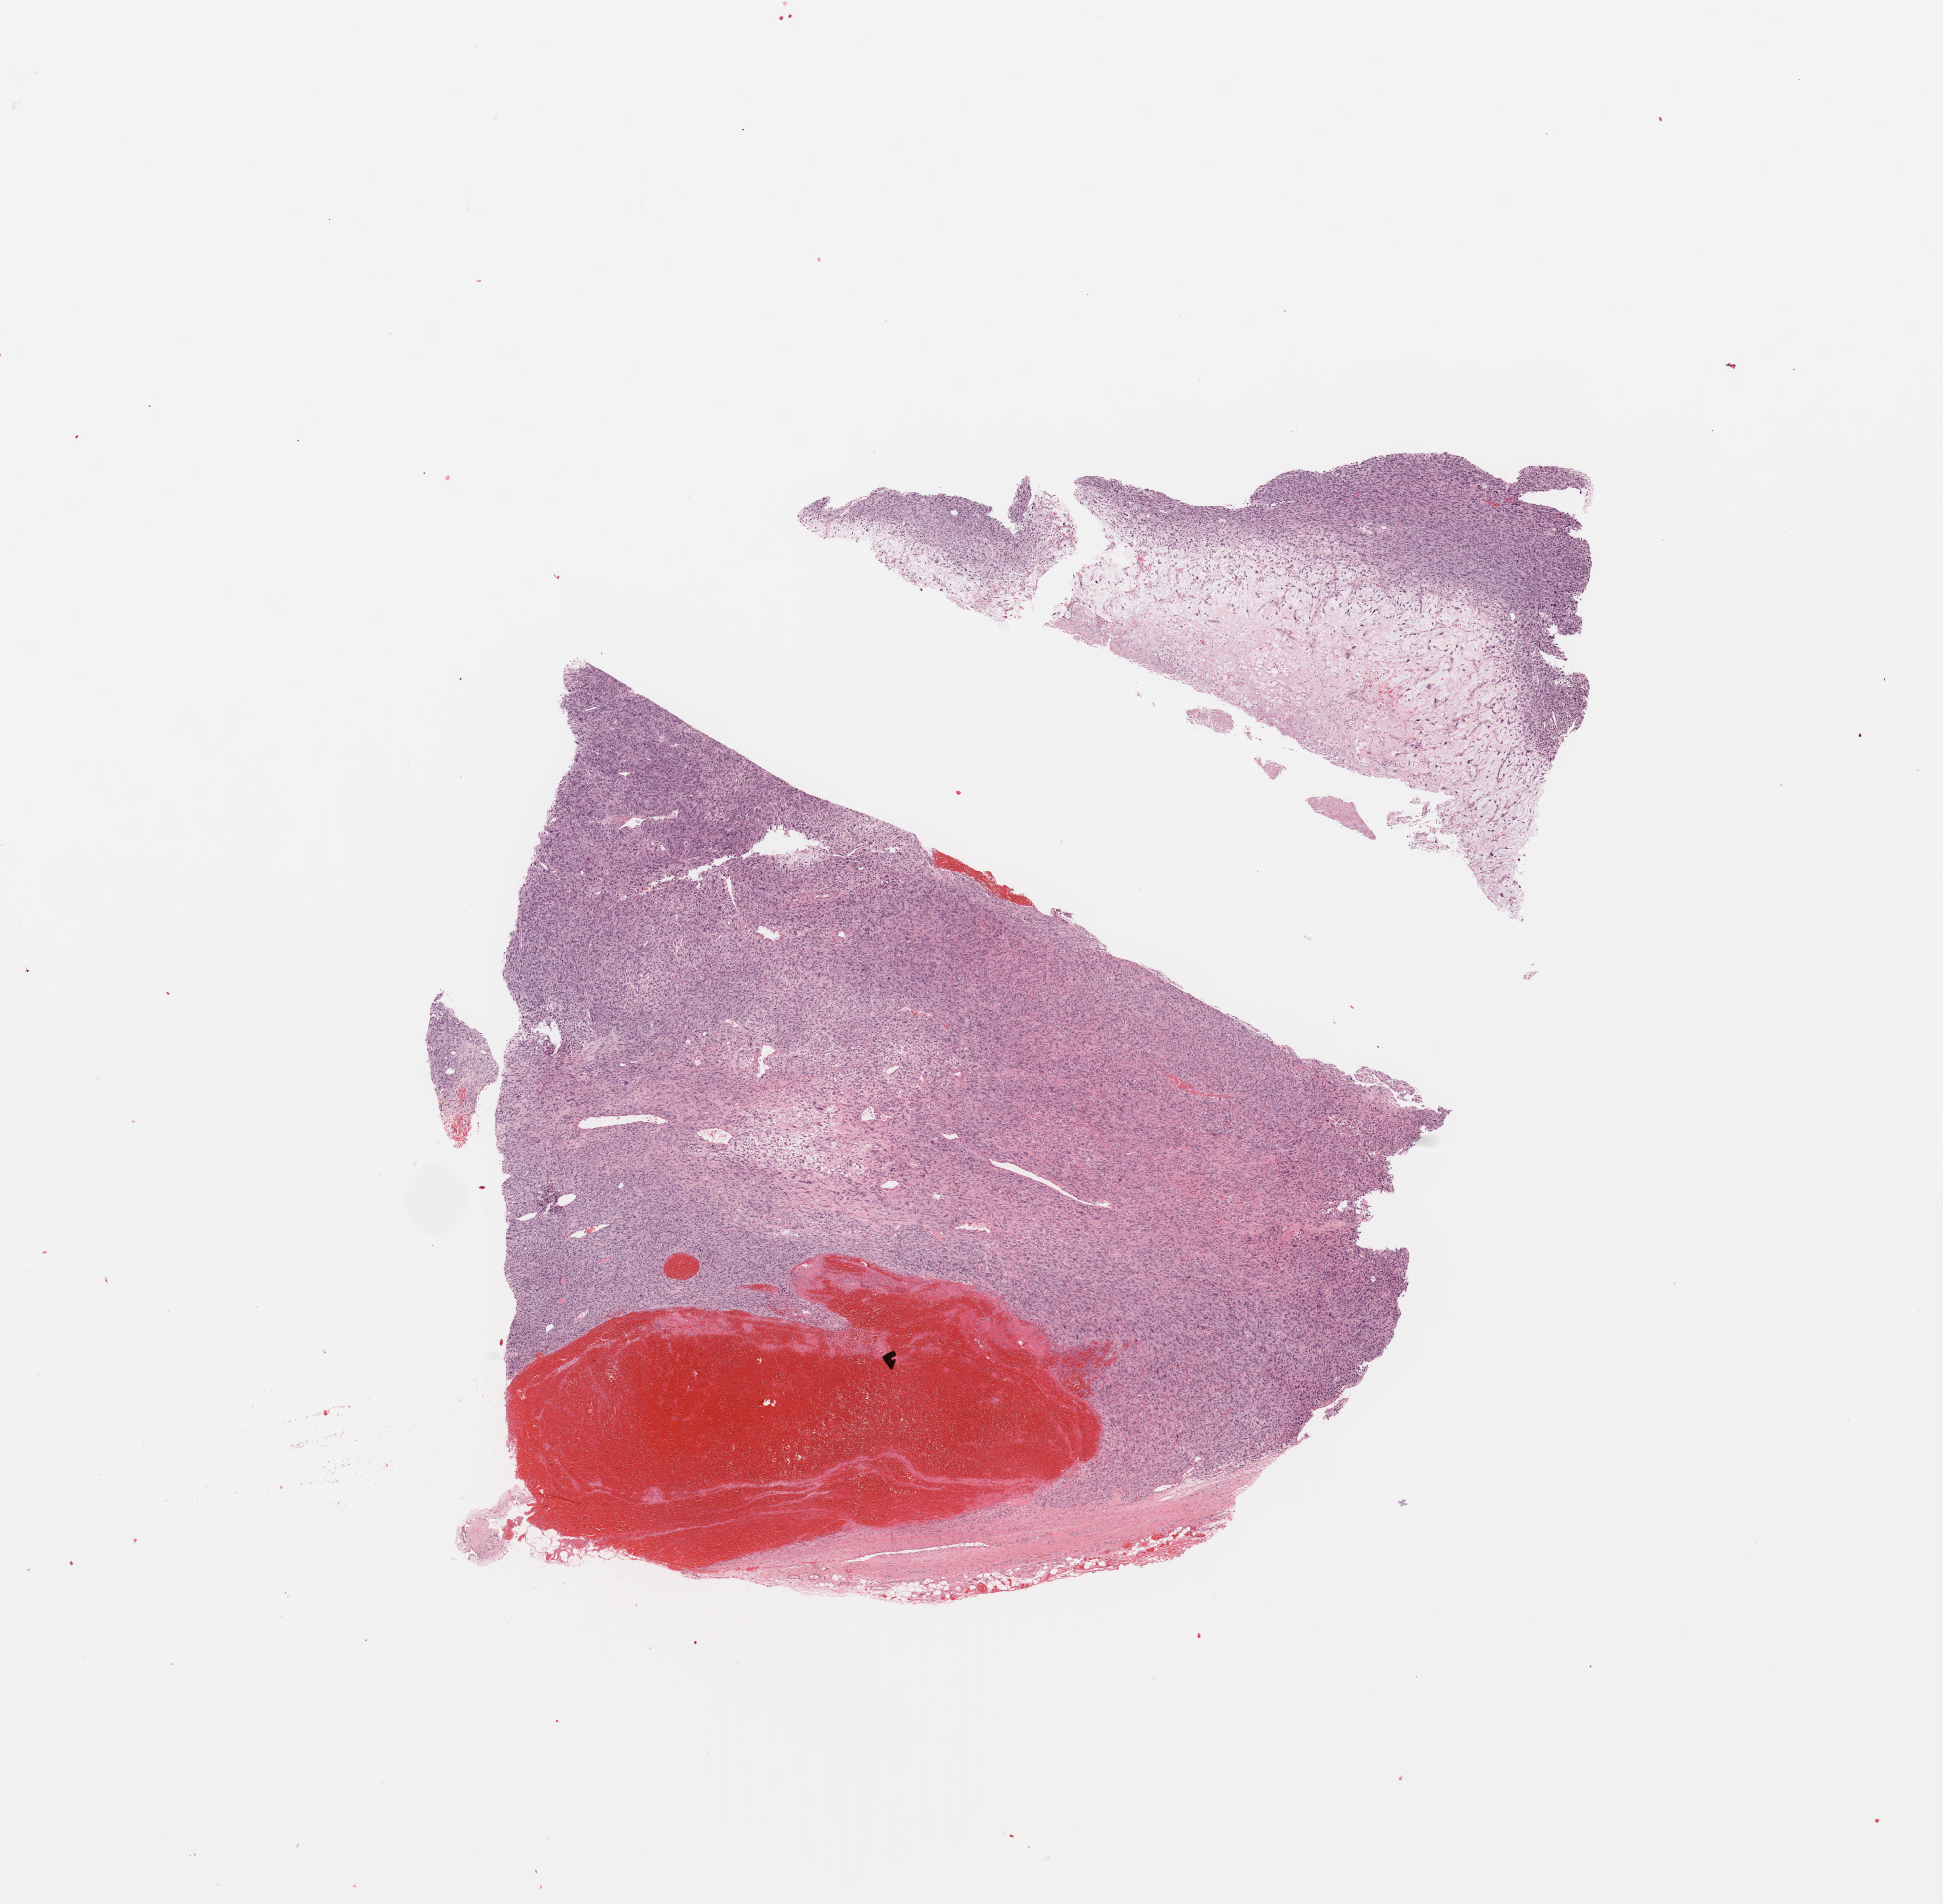
Digitized H&E tissue section (whole slide) — low-resolution overview of the scanned area, about 15.8 x 15.4 mm (acquisition: 20x scan), tumour tissue sample. Female, 88 y/o.
Patient diagnosis (cohort enrolment): sarcoma (site not recorded at cohort level). Primary tumour site (as recorded): lower extremity.